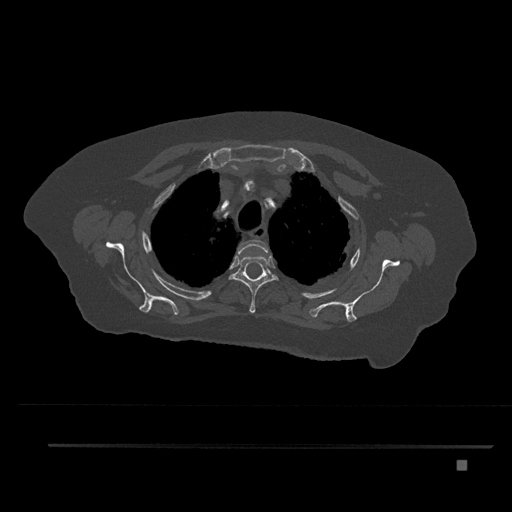
CT including the spine, one axial slice. Slice 640 of 797 in the series (ordered by position). Reconstruction kernel Br40s/3. Bone window (W 1800 / L 400 HU). 0.5 mm slice thickness. 512 × 512 image matrix. Patient: female, 76 years. Case-level facts recorded for this patient, not image findings: primary cancer: lung; vertebrae with lytic lesions (as recorded): T11, L3.
Structures marked on this image (semi-automatic segmentation, software-assisted and operator-edited):
- T2 vertebra: bounding box <237,239,270,257> (left, top, right, bottom; pixels)
- T3 vertebra: <228,256,279,313>